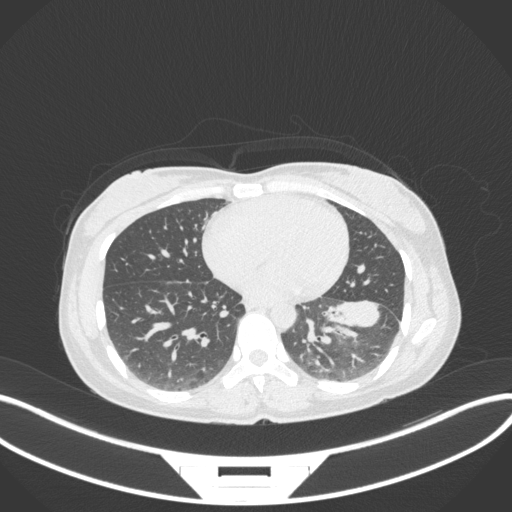
Chest CT, one axial slice; position 144 of 361 along the scan axis; lung window (W 1500 / L -600 HU); 512 × 512 image matrix, field of view 400 × 400 mm. Patient: female, 41 years. From the clinical record (not read from this slice): clinical TNM (as recorded): T2a N3 M1b.
Structures marked on this image (bounding box drawn by a radiologist):
- lung tumour (recorded histology: adenocarcinoma): bounding box <317,293,383,333> (left, top, right, bottom; pixels)